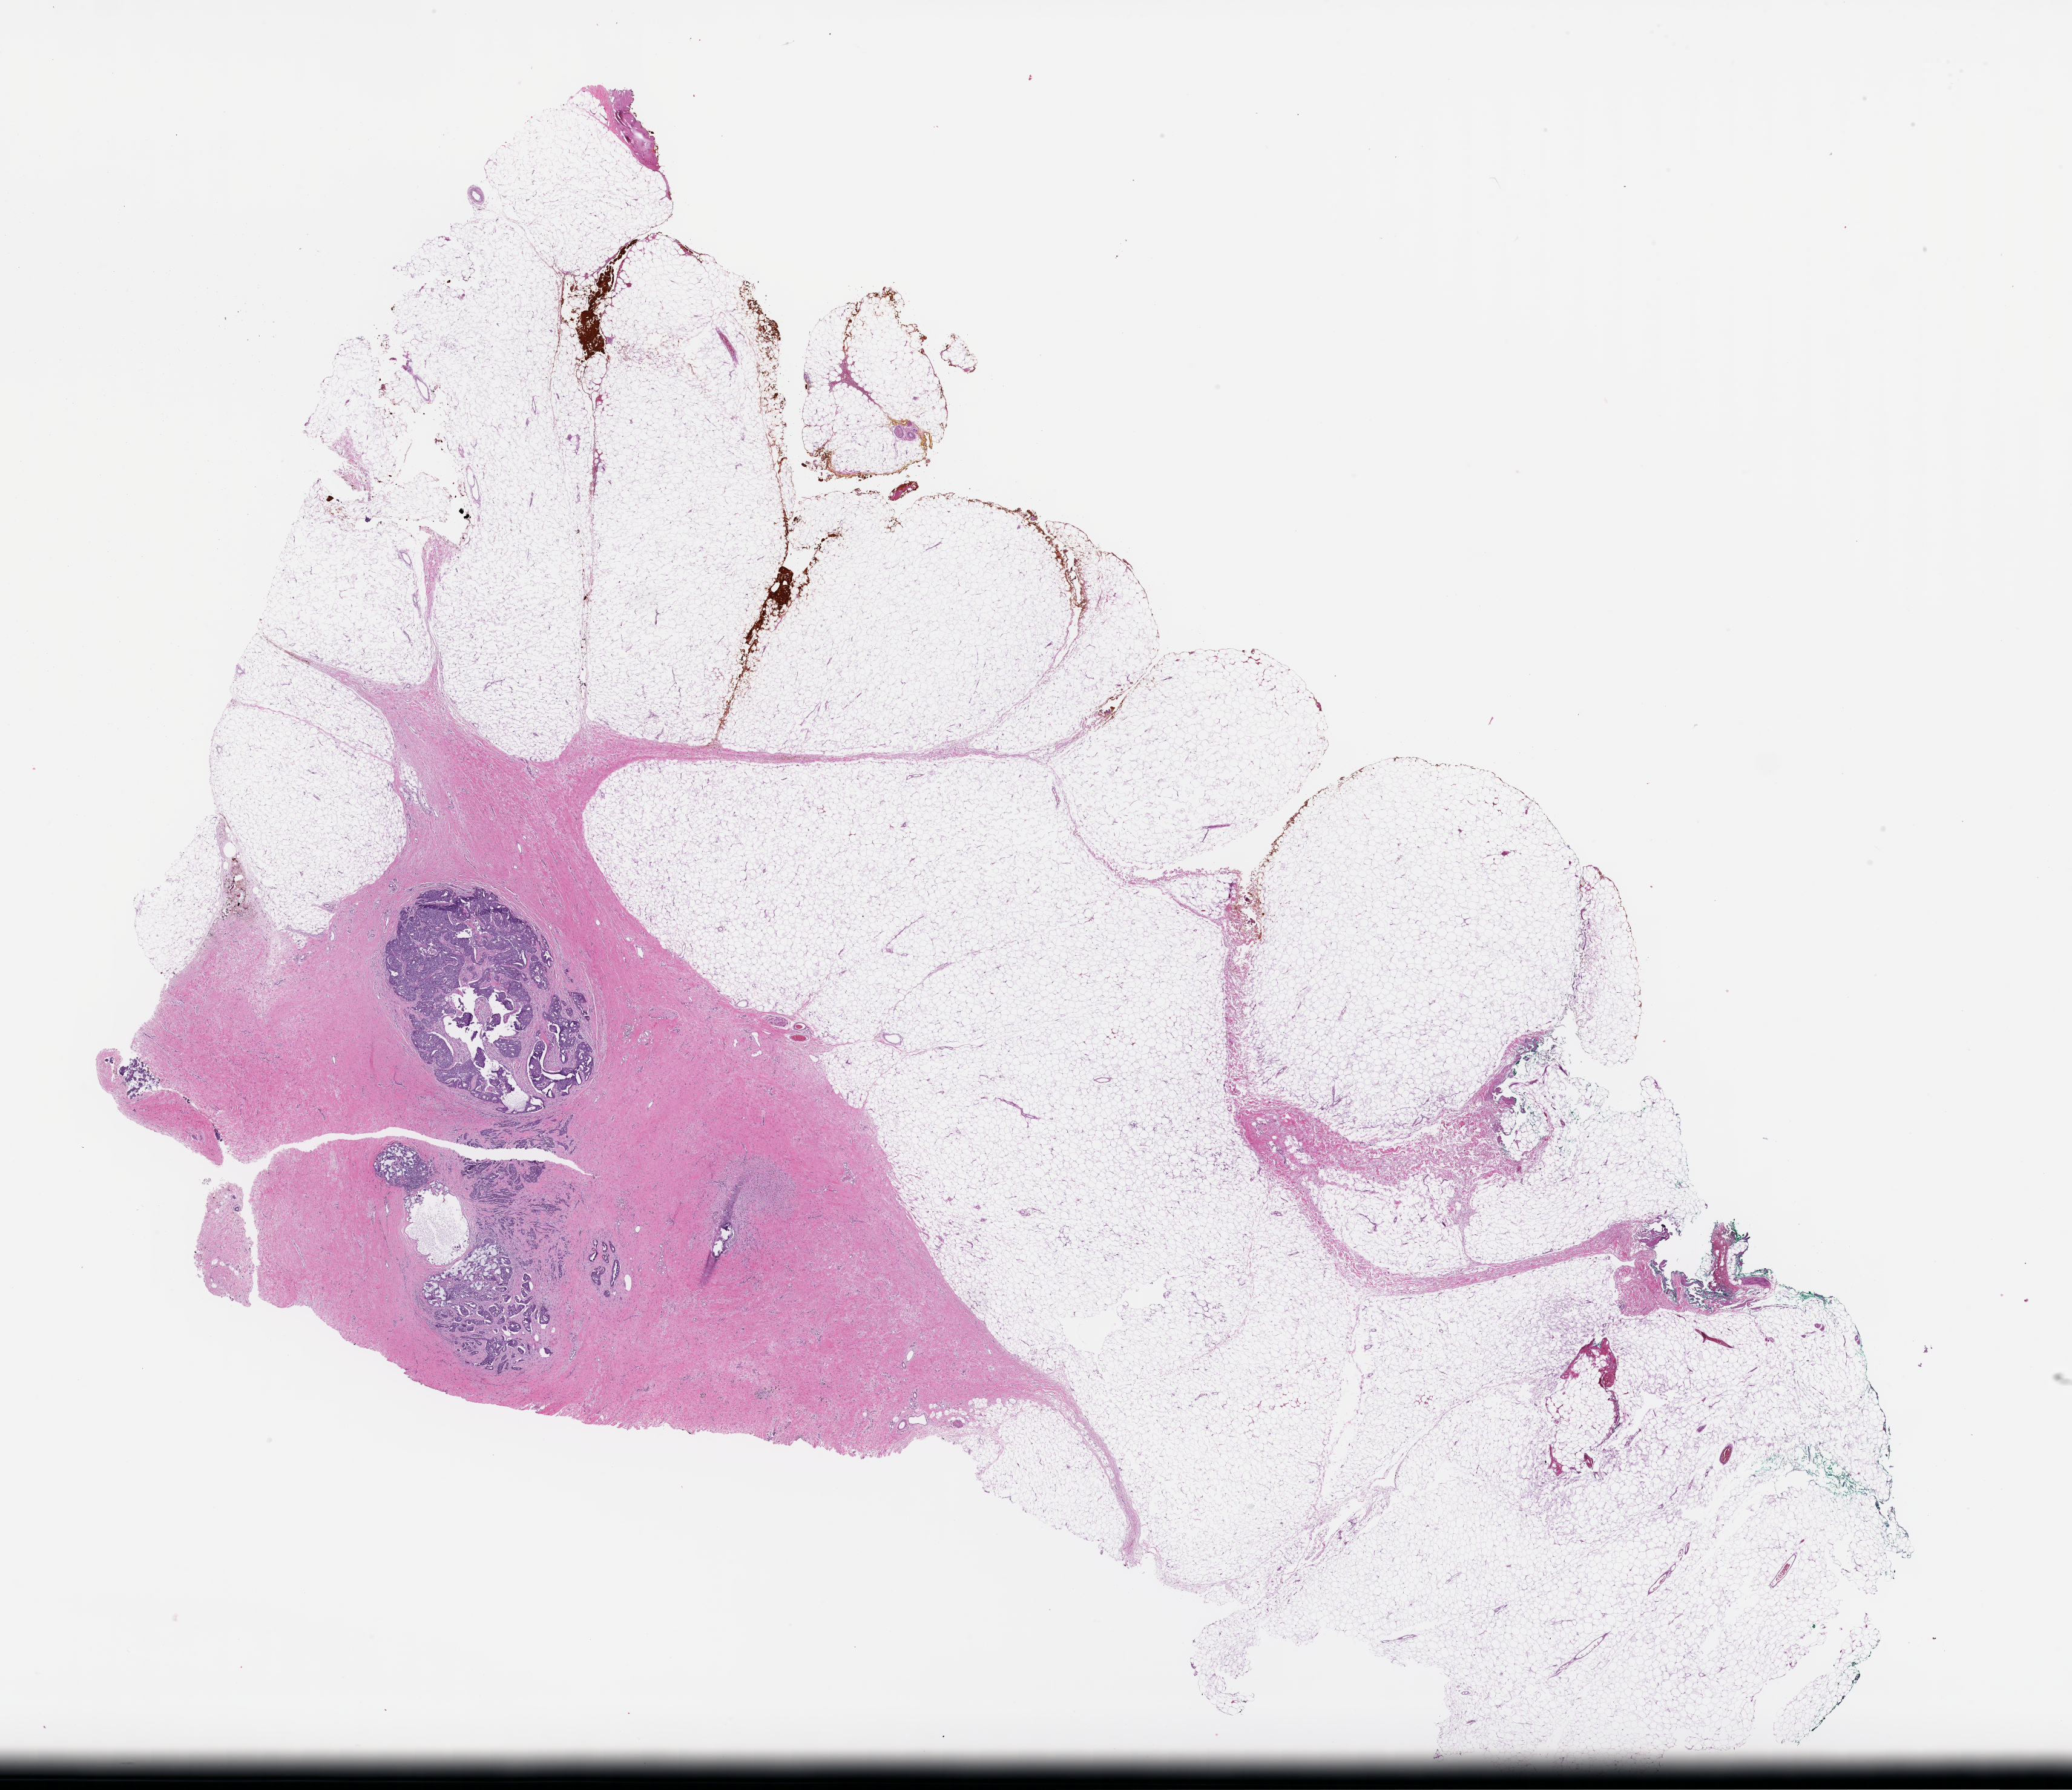
Hematoxylin and eosin (H&E) whole-slide image, low-resolution overview of the scanned area, about 27.6 x 23.9 mm. Formalin-fixed paraffin-embedded section. Tissue site: breast. Patient: female.
This section: primary tumour tissue. Diagnosis: Invasive Breast Carcinoma.